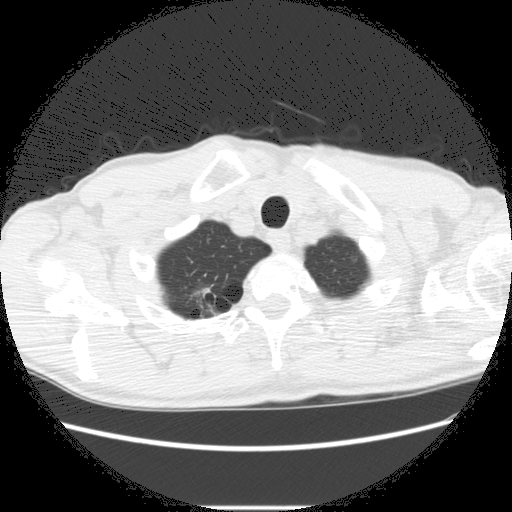
Chest CT (low-dose screening protocol), one axial image. Second annual screen. Lung window (W 1500 / L -600 HU). Standard (soft-tissue) reconstruction kernel (STANDARD). 120 kVp. 512 × 512 image matrix. Male participant, aged 66 years at enrolment.
Expert-annotated lung lesion, box from (x=170, y=275) to (x=236, y=328) px. The screening reader recorded 5 non-calcified nodules or masses ≥4 mm on this exam (right lower lobe, right upper lobe, right upper lobe, right upper lobe, left lower lobe); which of them this box marks is not recorded. Official screen result: positive, change unspecified: nodule(s) >= 4 mm or enlarging nodule(s), mass(es), or other non-specific abnormalities suspicious for lung cancer. Lung cancer was diagnosed 75 days after this screen: adenocarcinoma, NOS, right upper lobe, undifferentiated (G4), stage IA (AJCC 6th edition), 20 mm at pathology.